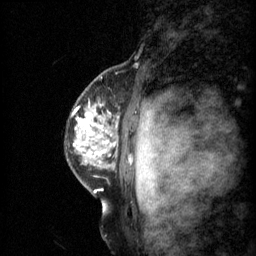
Breast MRI (dynamic contrast-enhanced), one sagittal slice. Position 47 of 60 along the scan axis. 3 images stored at this slice position (order not interpretable as contrast timing). 1.5 T. TE 4.2 ms, TR 11 ms. 256 × 256 image matrix, field of view 200 × 200 mm. Female patient, age 48 years.
Structures marked on this image (semi-automatic segmentation, software-assisted and operator-edited):
- analysis volume of interest (the breast-tissue region the enhancement analysis was run in; not a lesion): bounding box (x1, y1, x2, y2) in pixels: (74, 74, 139, 147)
- tumour enhancement mask (voxels above the 70 % enhancement threshold inside the analysis volume of interest): (74, 110, 118, 147)